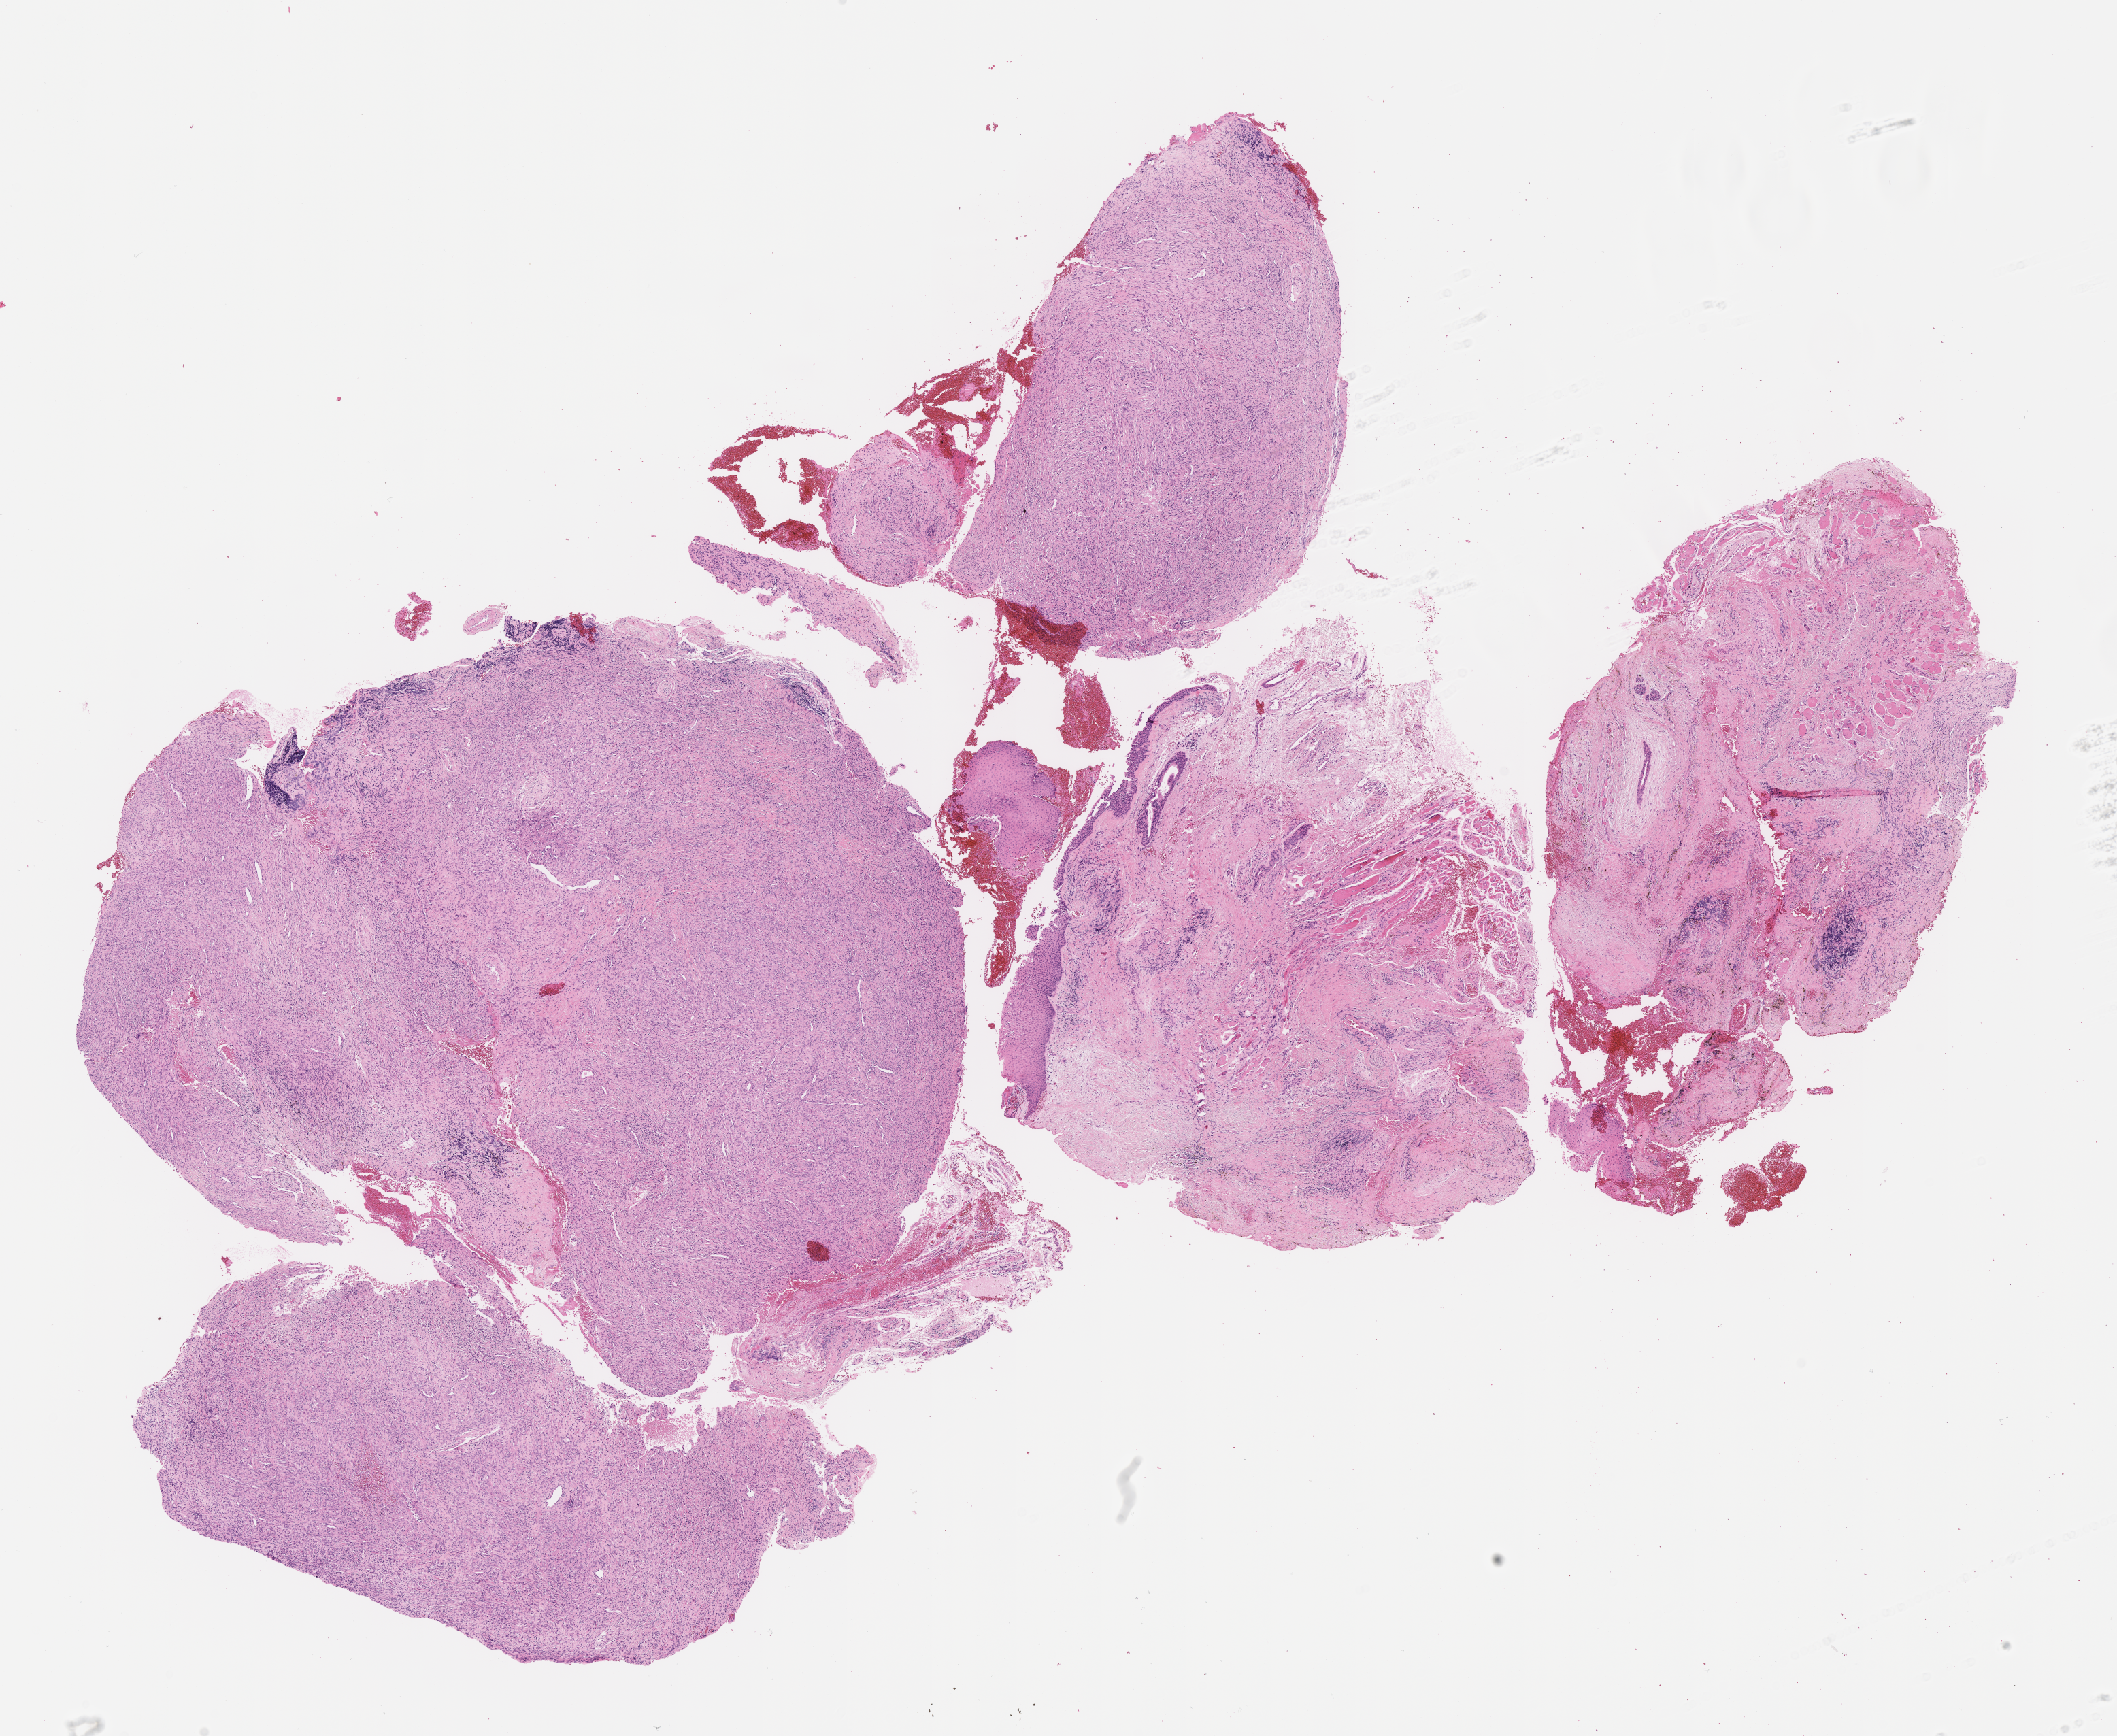
H&E whole-slide image of tumor tissue — a low-resolution overview of the entire scanned area, about 12.6 x 10.3 mm. Formalin-fixed paraffin-embedded section. Patient: male, age 45.2 years at diagnosis.
* stage (as recorded): 1
* metastatic status at presentation (as recorded): non-metastatic
* diagnosis: rhabdomyosarcoma; histological classification: spindle cell rhabdomyosarcoma